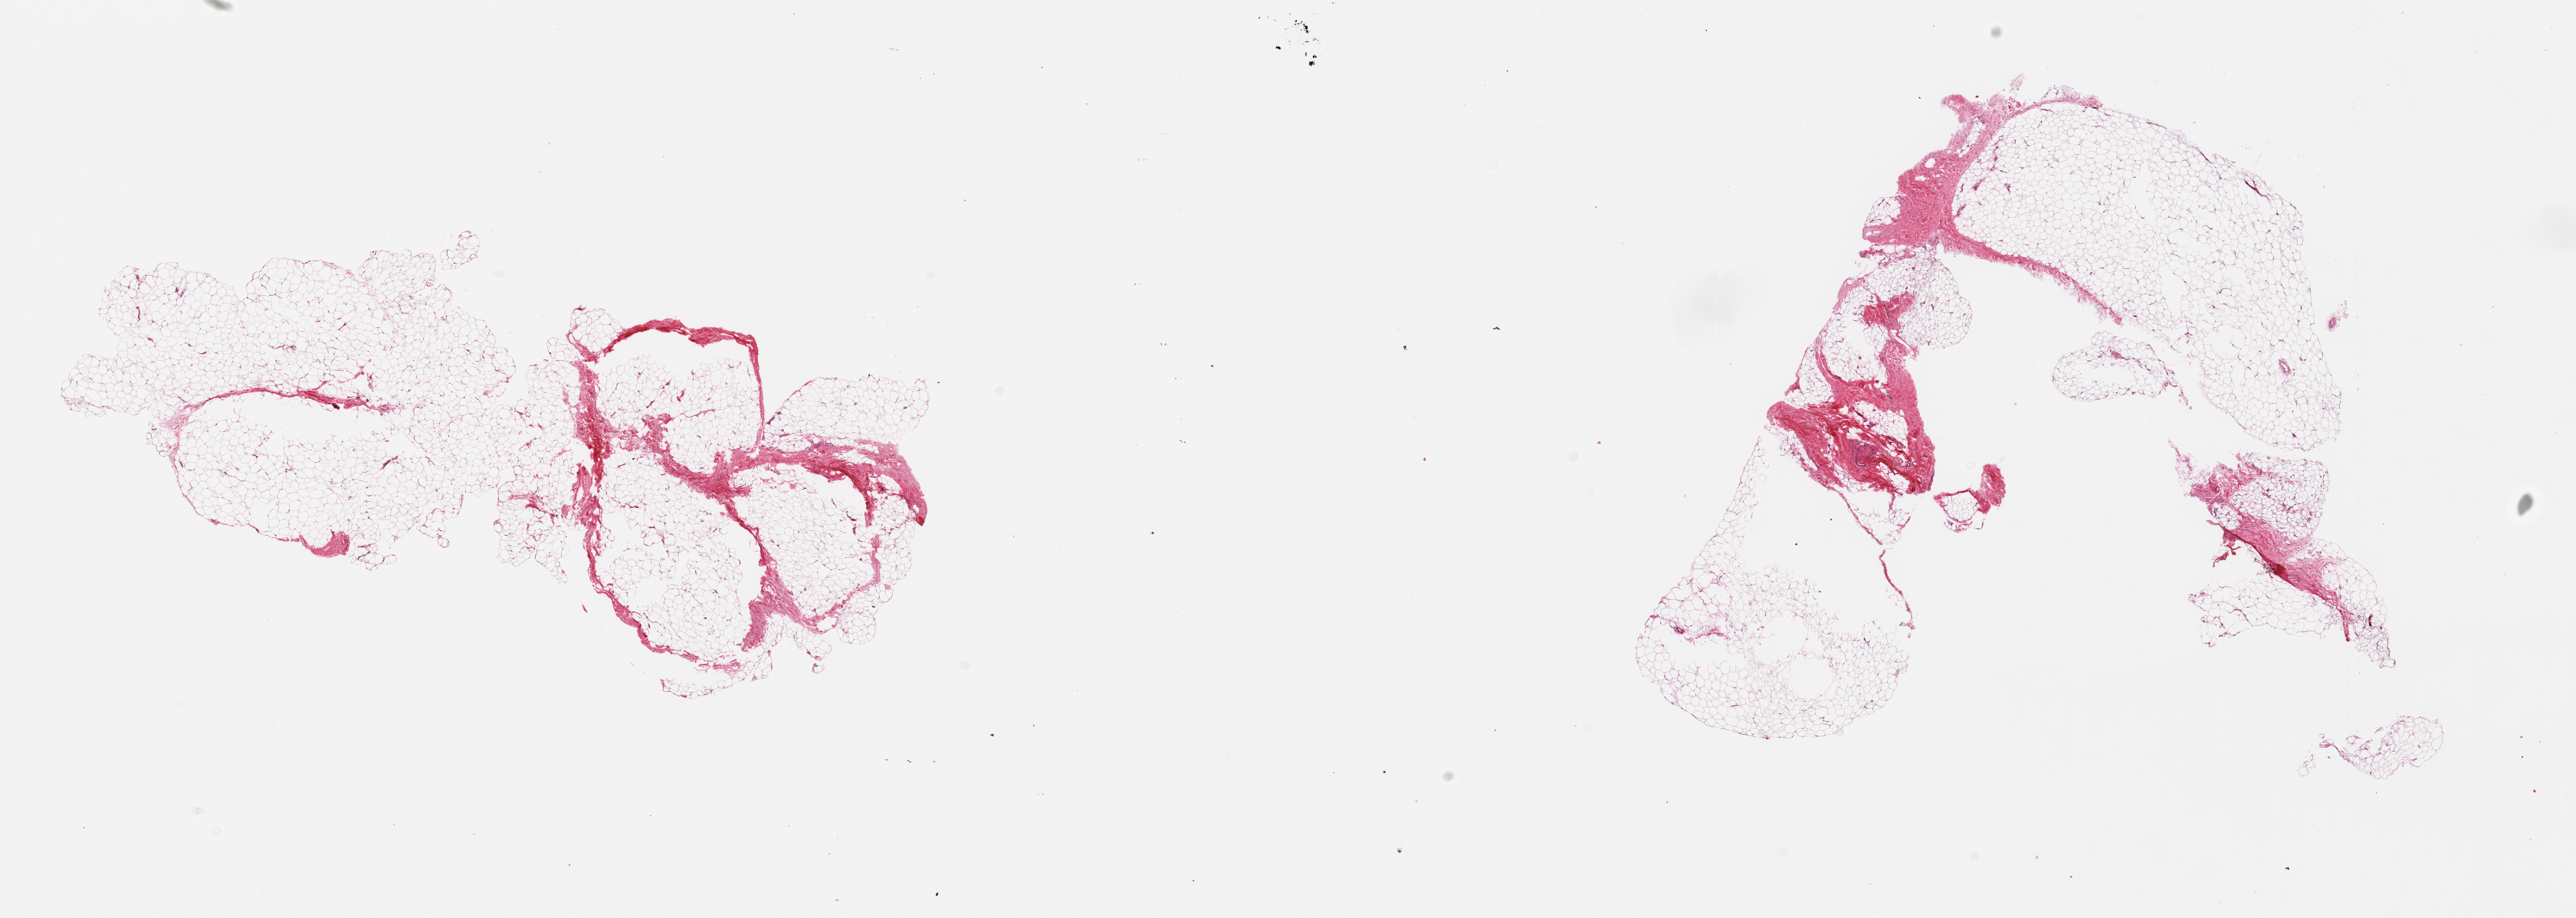
H&E whole-slide image — low-resolution overview of the scanned area, about 26.6 x 9.5 mm (slide scanned at 20x), PAXgene-fixed paraffin-embedded (PFPE) section, target tissue: adipose tissue, donor tissue sample.
* reviewer comment on this tissue sample: 2 pieces; 1 has 10% fibrous content